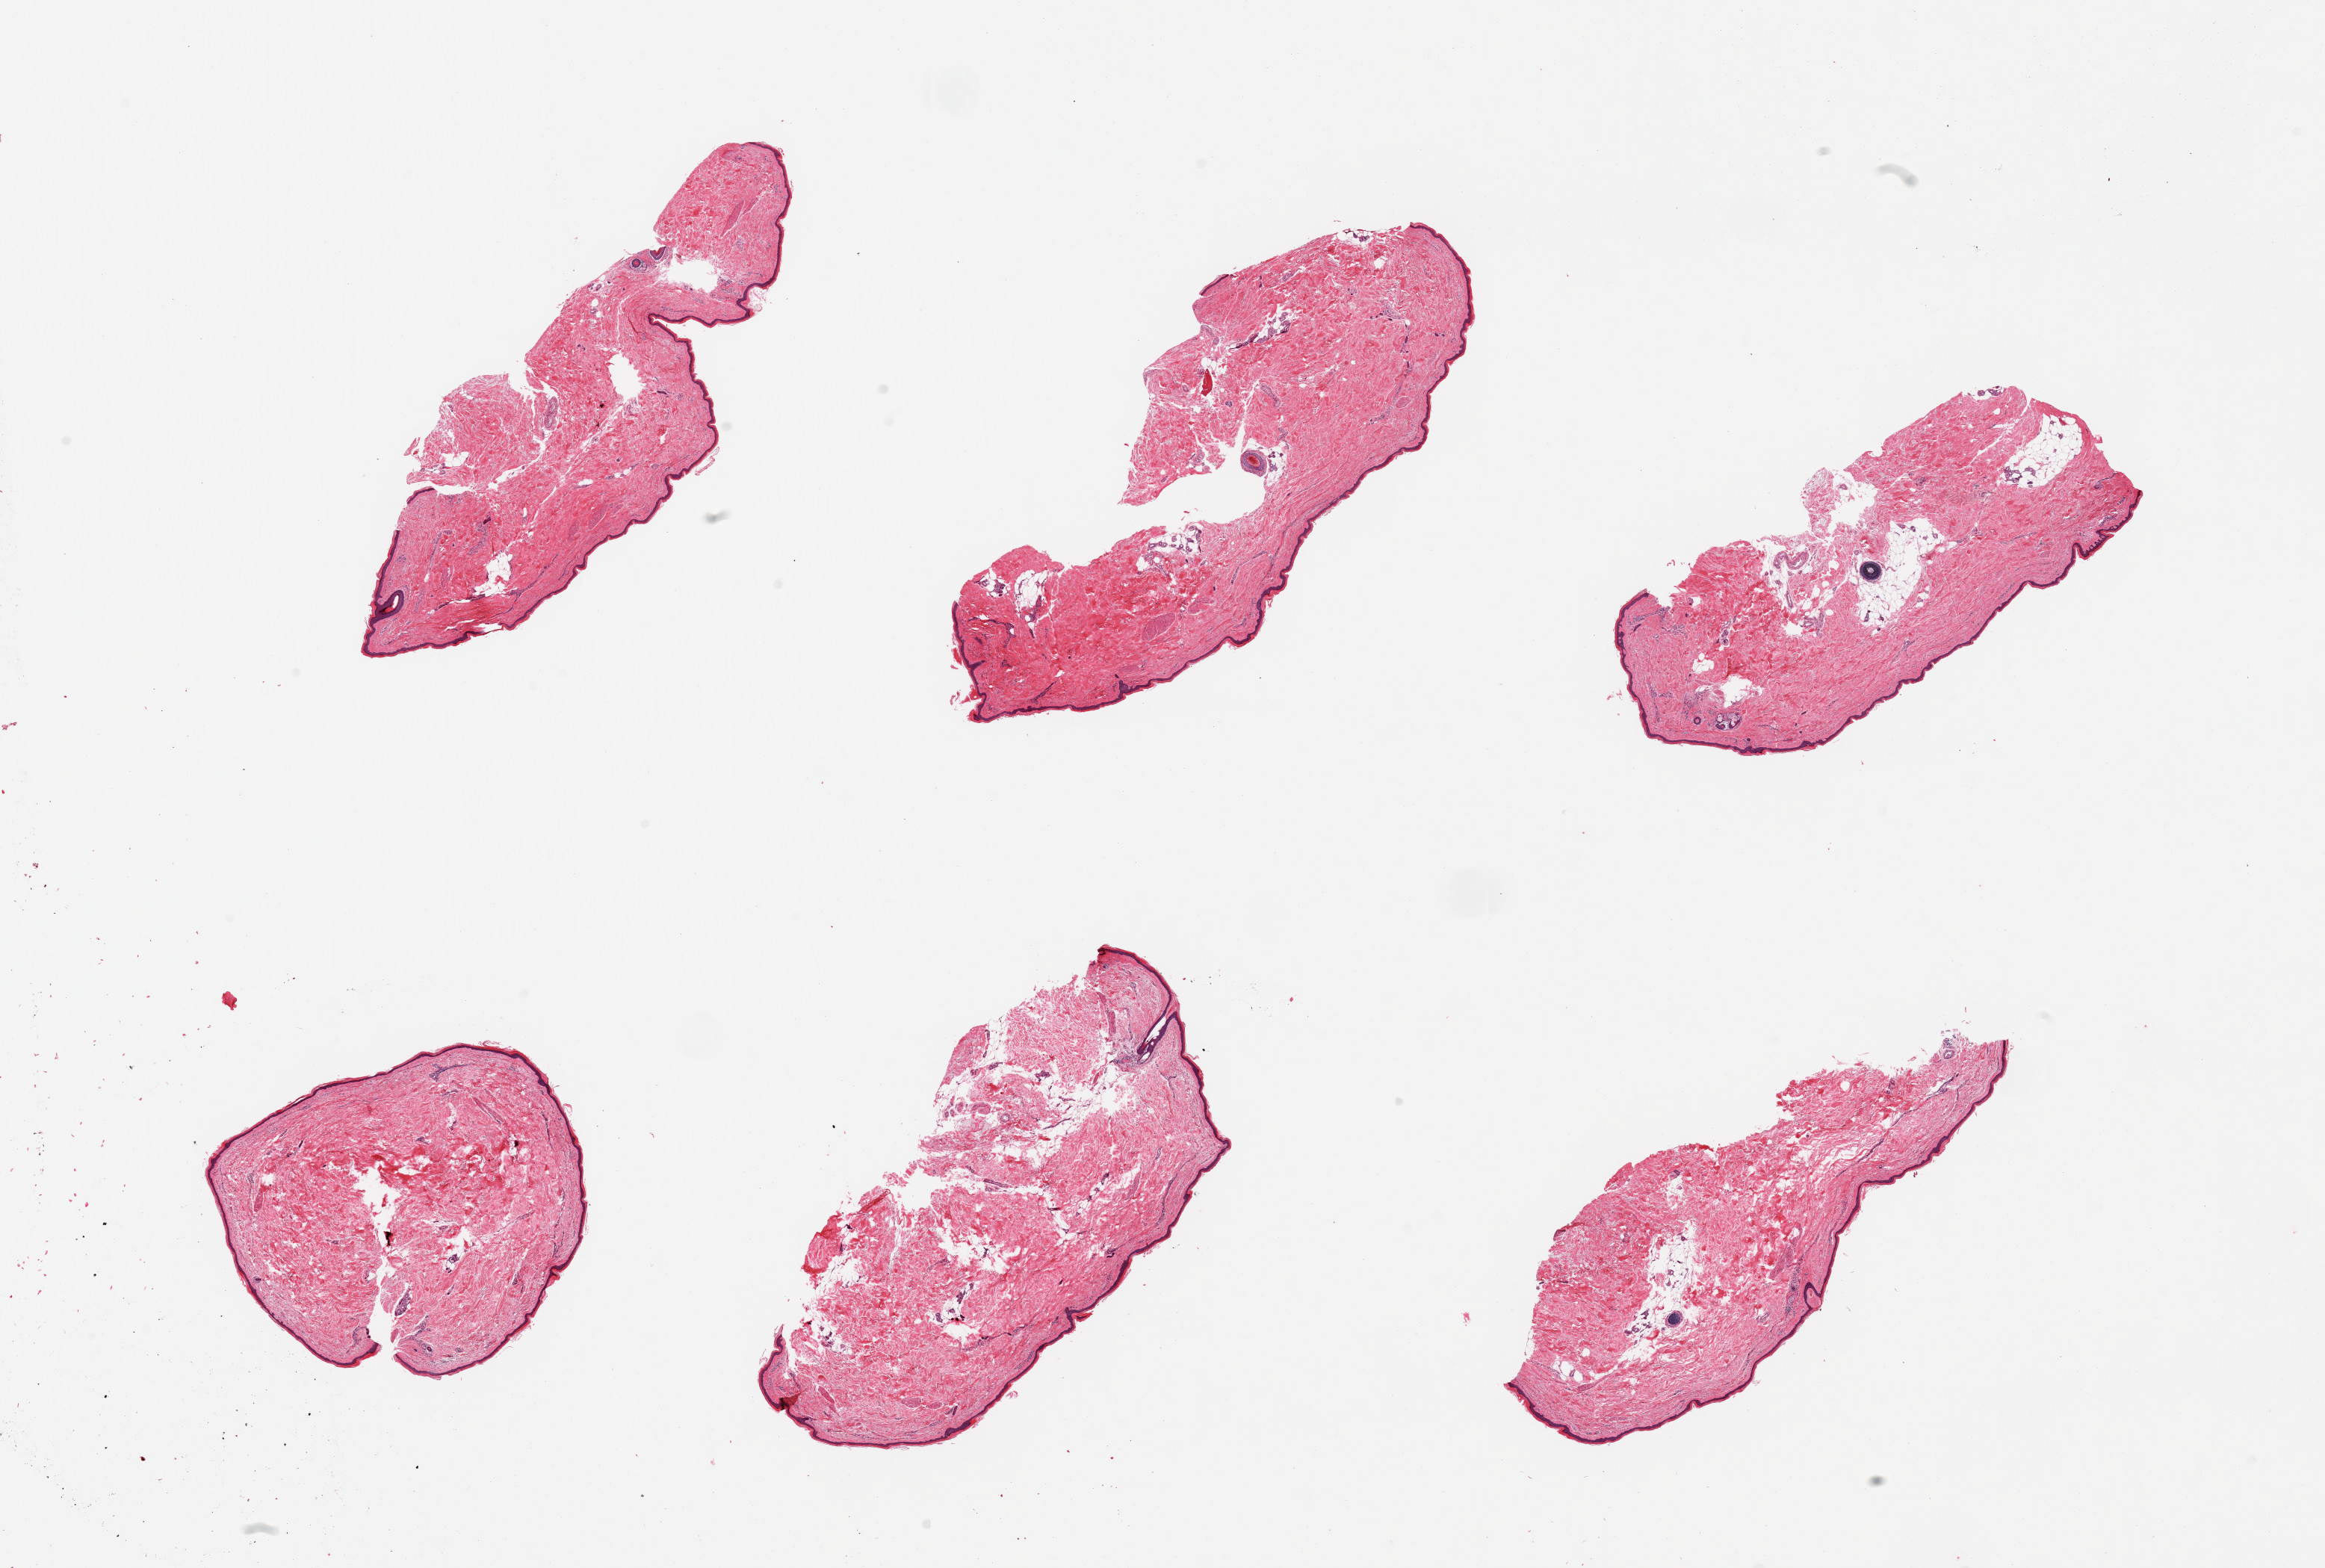
Digitized H&E-stained section, low-resolution overview of the scanned area, about 24.6 x 16.6 mm (from a 20x scan); PAXgene-fixed paraffin-embedded (PFPE) section; sampled site (target tissue): skin of lower leg; donor tissue sample. Donor: female.
- review note (as recorded): 6 pieces; well trimmed; up to 20% intradermal fat